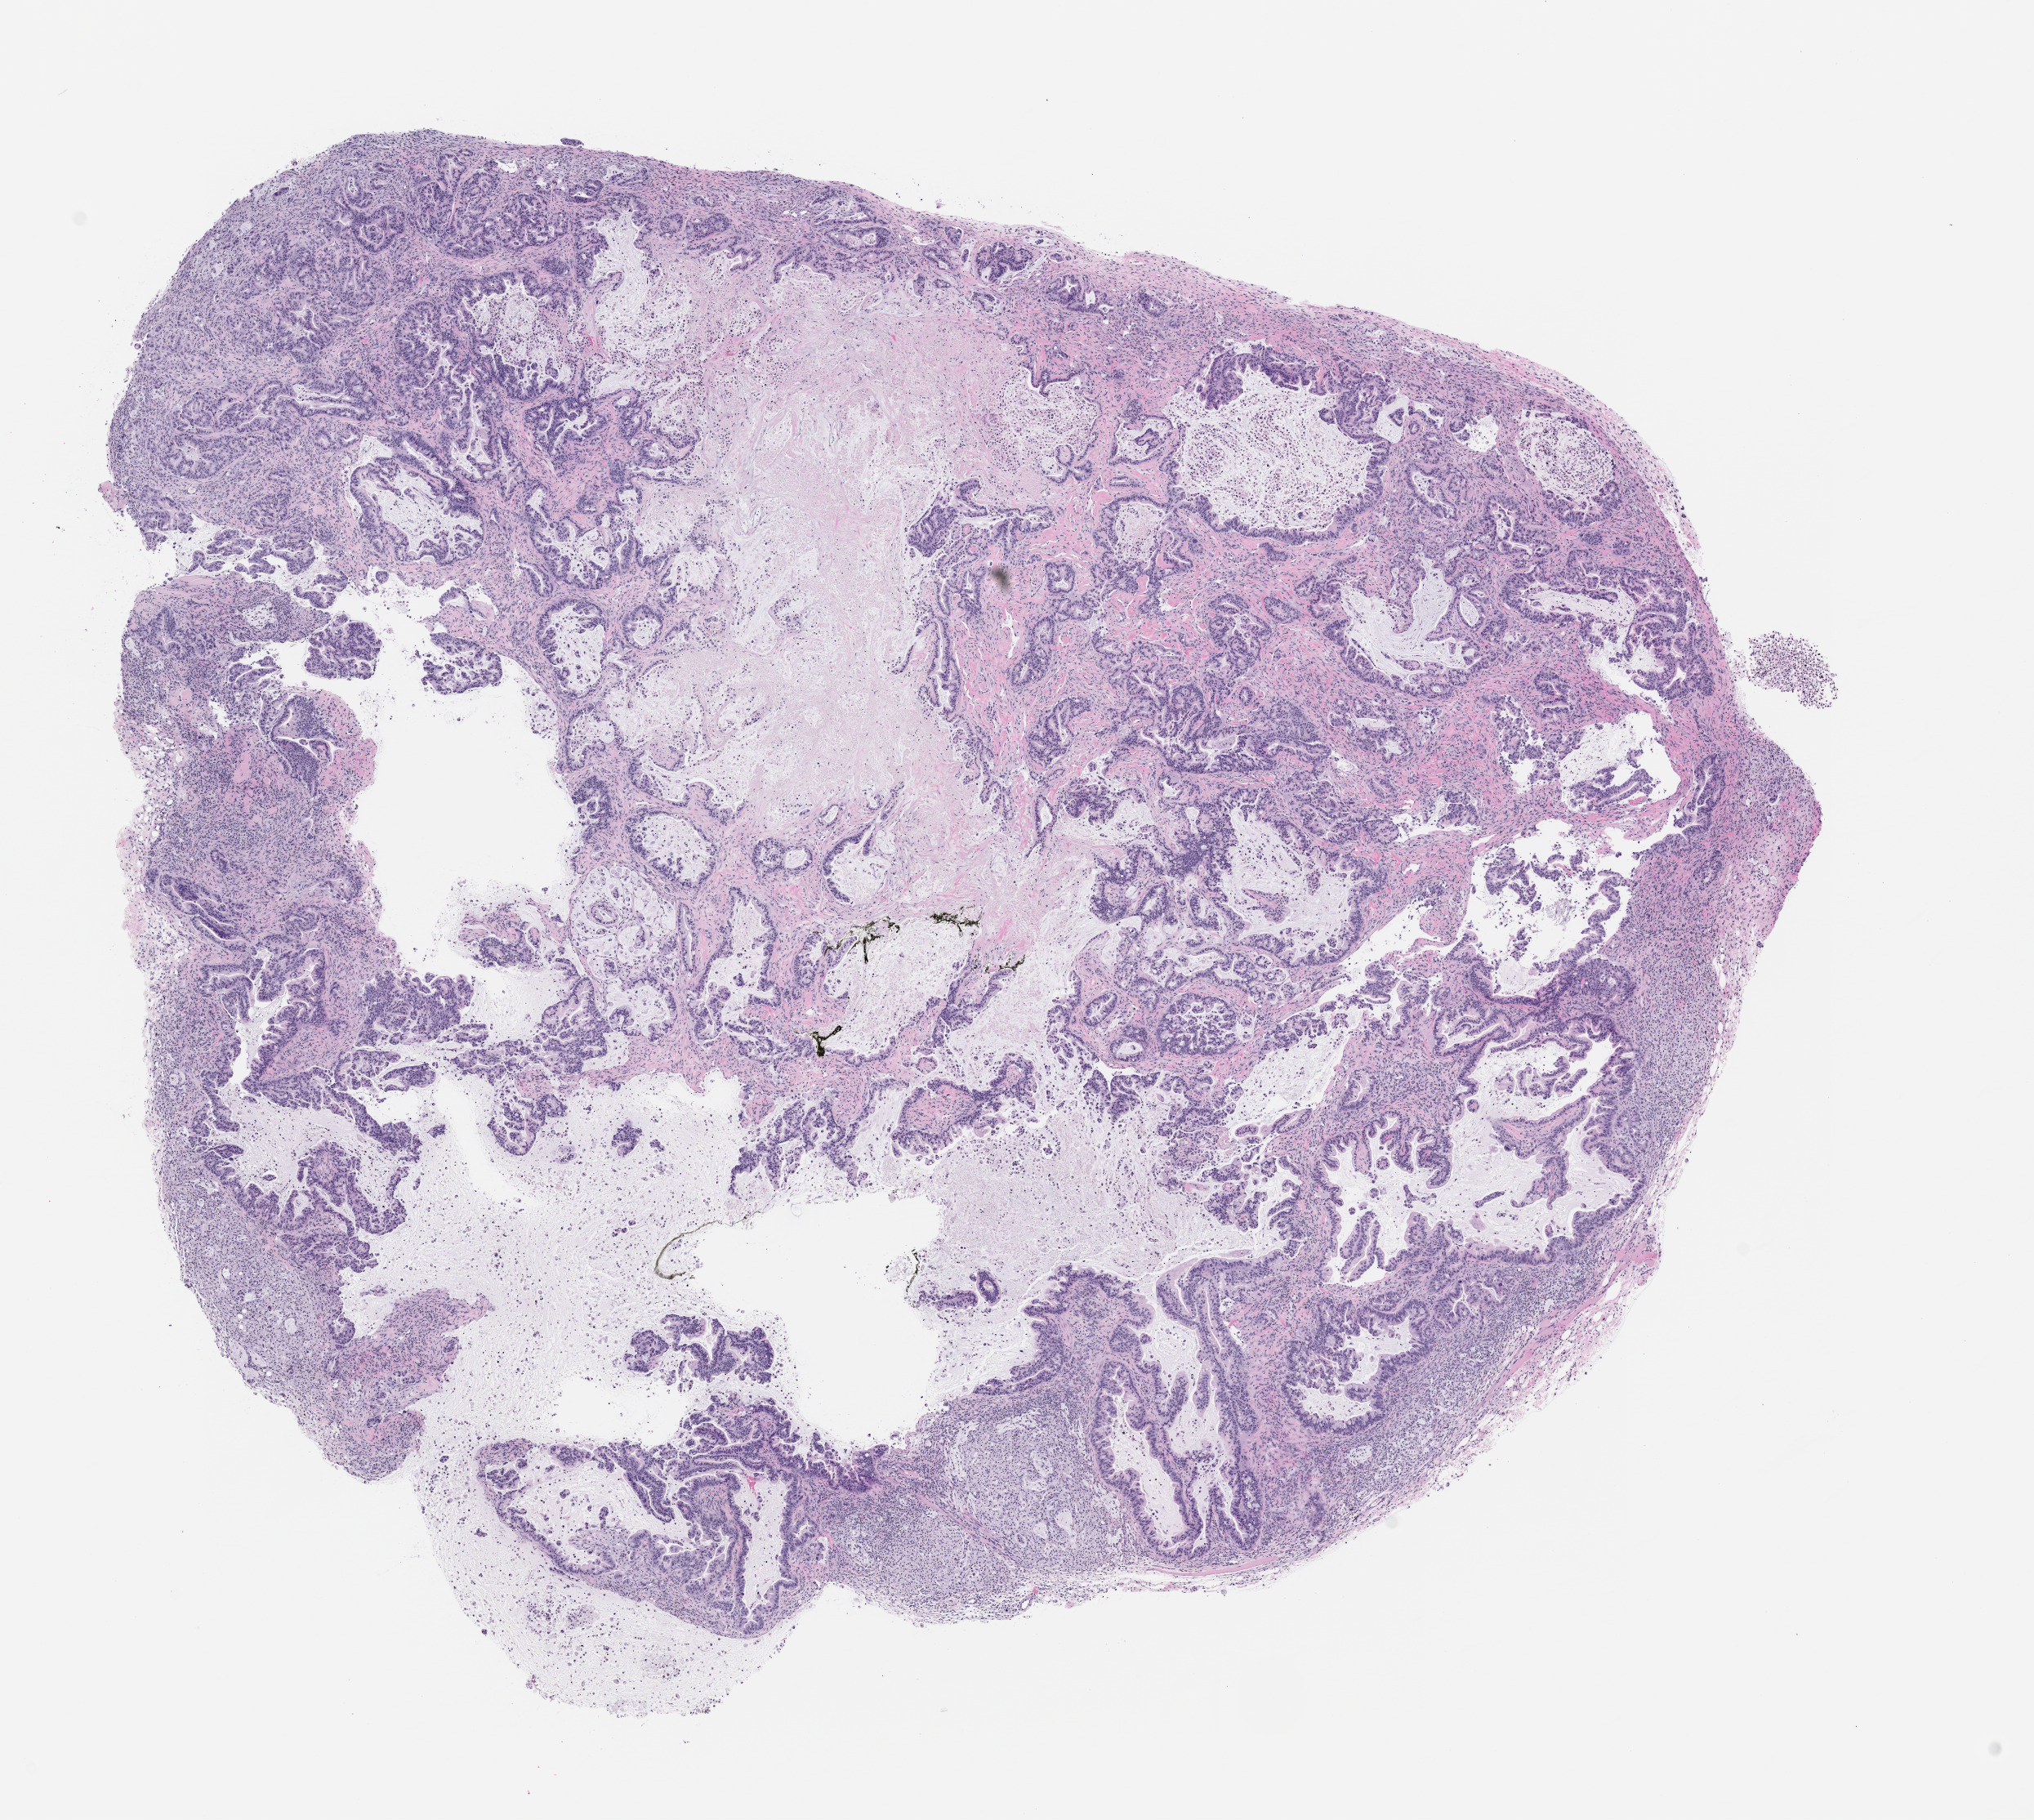
Hematoxylin and eosin (H&E) whole-slide image of a patient-derived xenograft (PDX) tumor grown in a mouse, passage 1, low-resolution overview of the scanned area, about 10.0 x 9.0 mm. FFPE section. Originating tumor site category: pancreas.
Originating patient diagnosis: Pancreatic Adenocarcinoma.